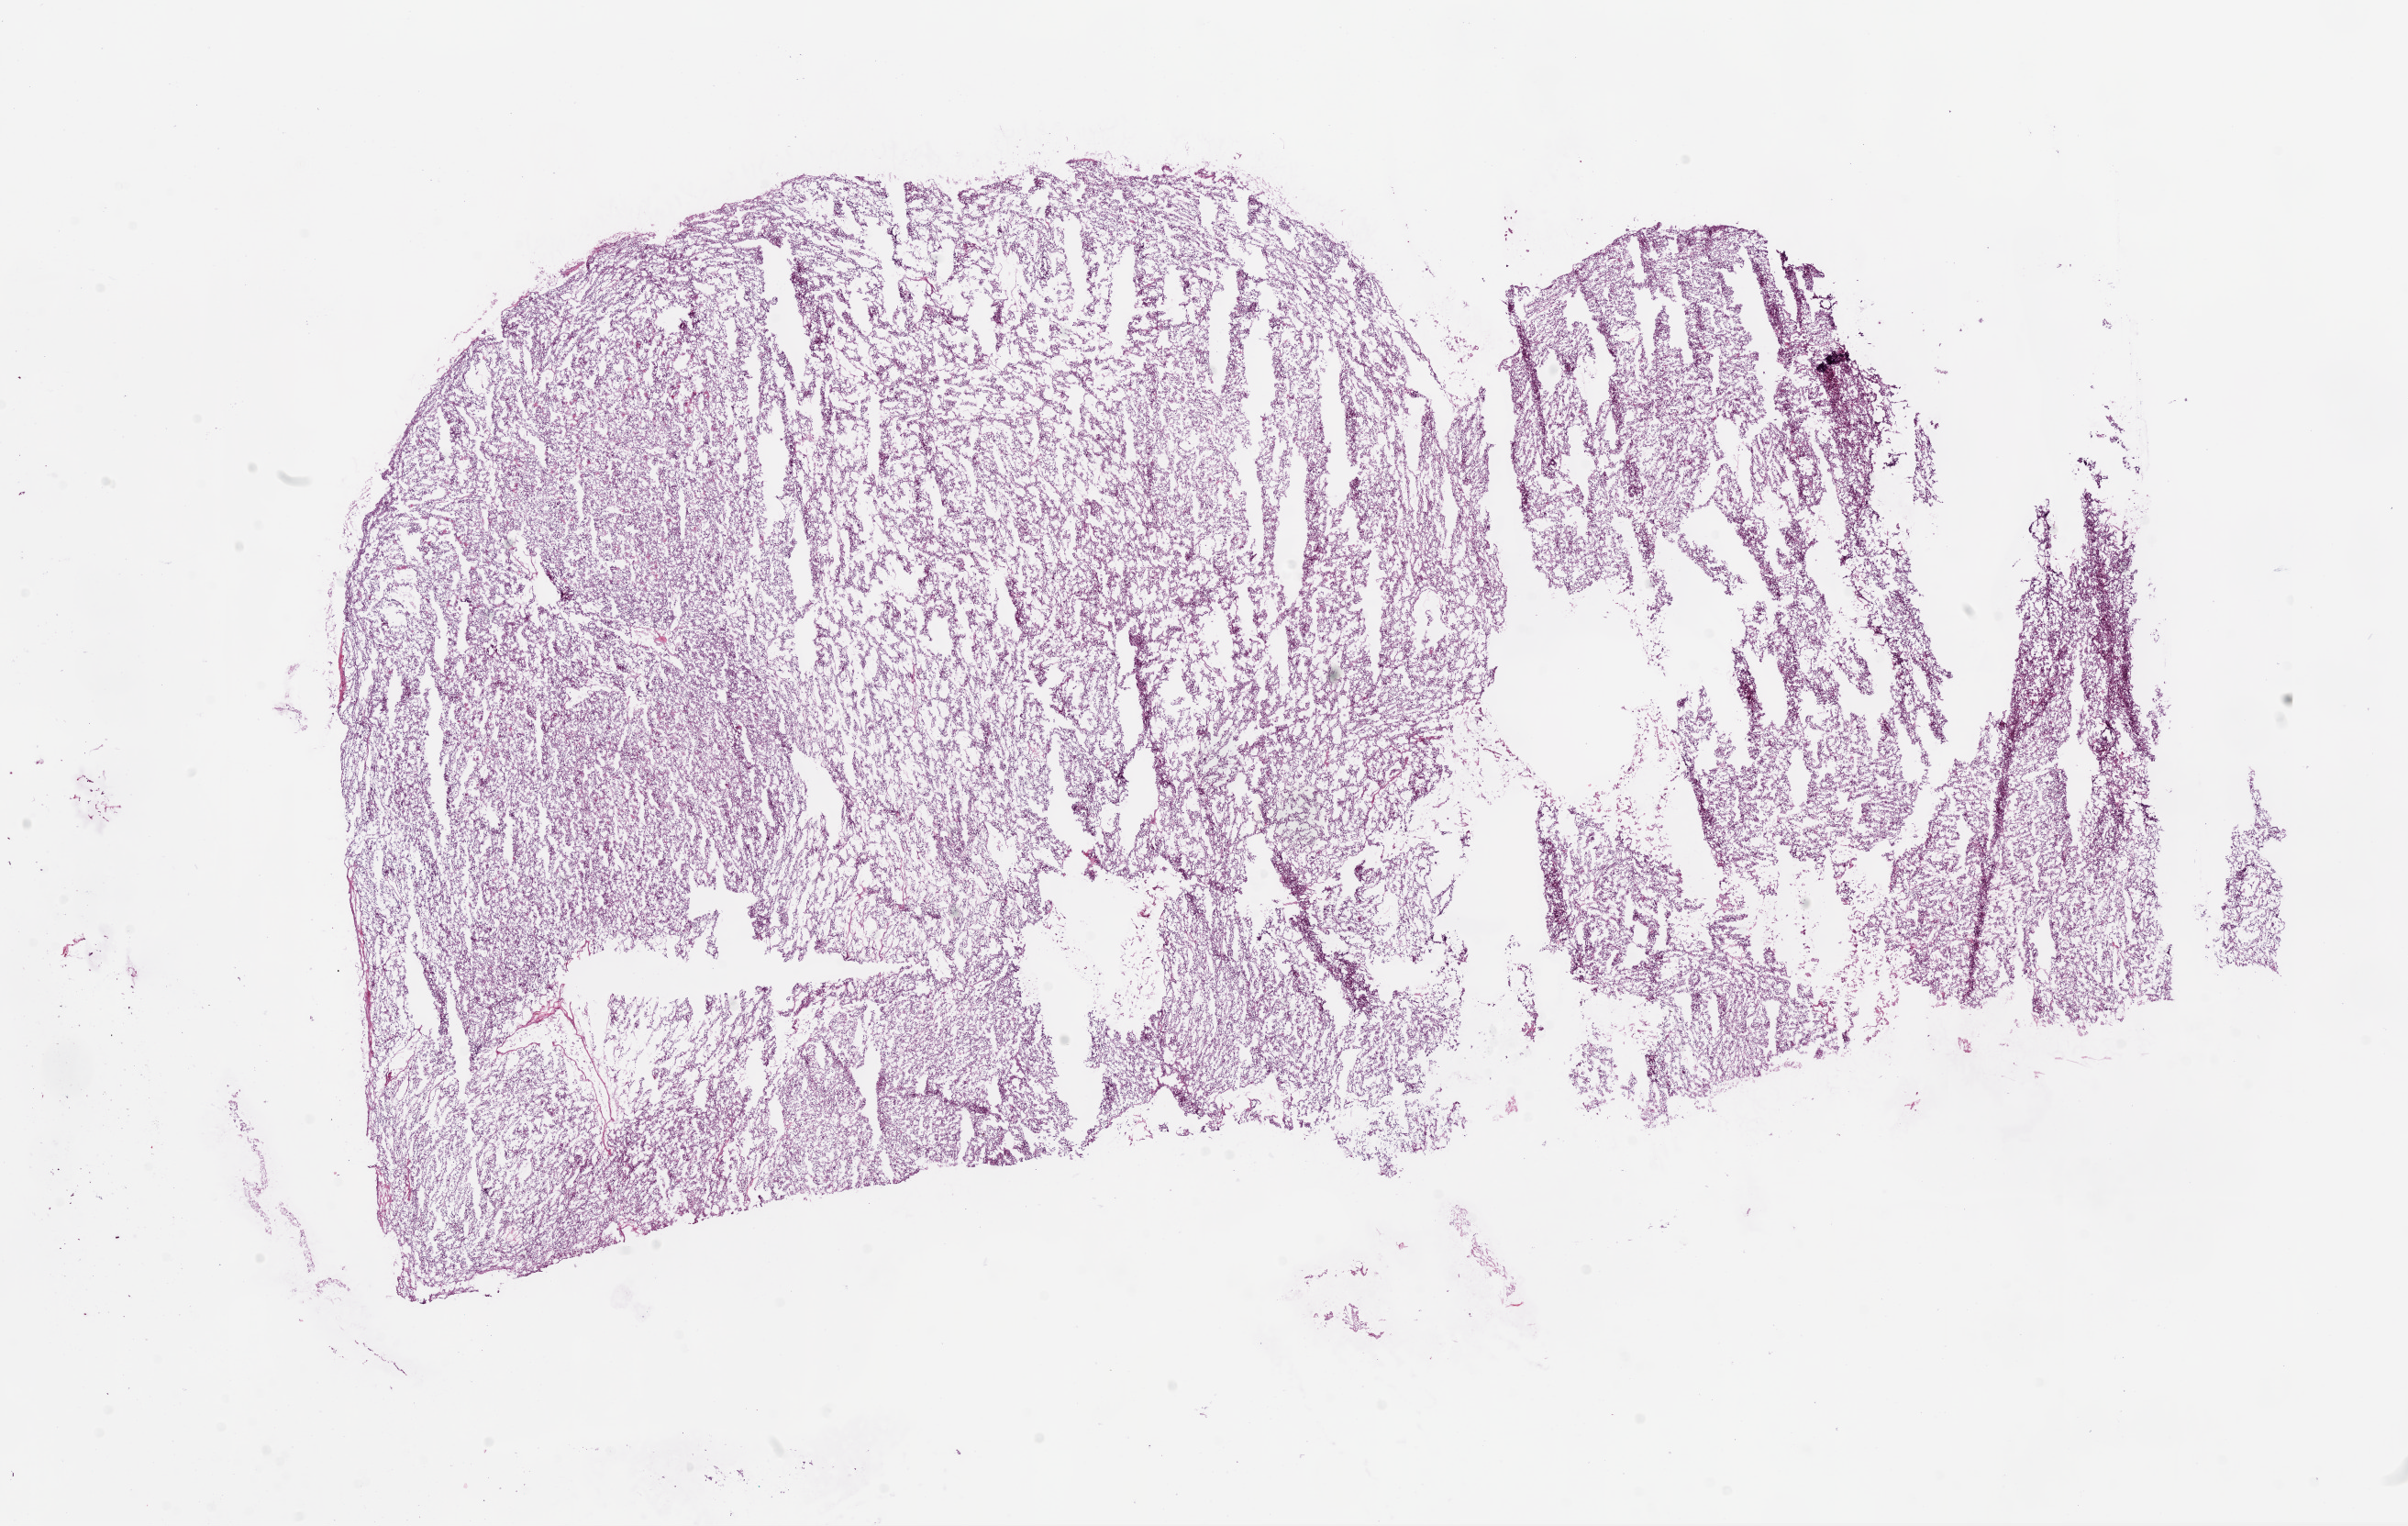
Digitized H&E-stained tissue section (whole slide), whole scanned area (about 21.1 x 13.3 mm) shown as a low-resolution overview; frozen section; primary tumour sample from the kidney. Female patient; age at initial diagnosis 80 years. Histologic grade: G2 (moderately differentiated). Pathologist review of this section (percent, as recorded): tumour cells 93%, tumour nuclei 85%, normal cells 0%, stromal cells 5%, necrosis 2%.
Laterality: left. AJCC pathologic stage: I. Pathologic diagnosis: Clear cell adenocarcinoma, NOS.